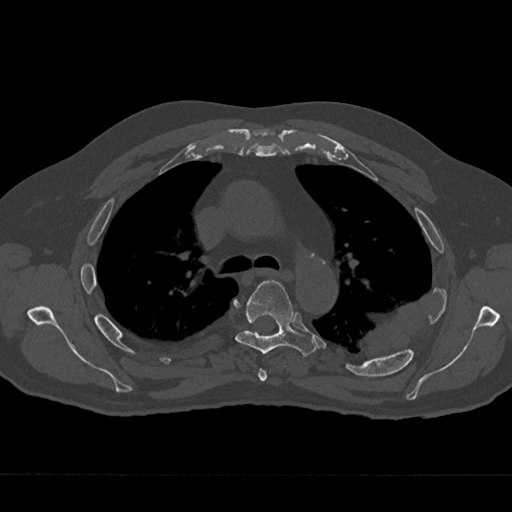
CT including the spine, one axial slice. Reconstruction kernel Br40s/3. 120 kVp. Bone window (W 1800 / L 400 HU). 0.5 mm slice thickness. 512 × 512 image matrix, field of view 377 × 377 mm. Male patient, age 75 years. Case-level facts recorded for this patient, not image findings: primary cancer: renal; vertebrae with lytic lesions (as recorded): T4.
Outlined on this slice (semi-automatically segmented with operator editing):
- T4 vertebra: bounding box [x1, y1, x2, y2] px = [258, 368, 267, 382]
- T5 vertebra: [235, 280, 317, 356]